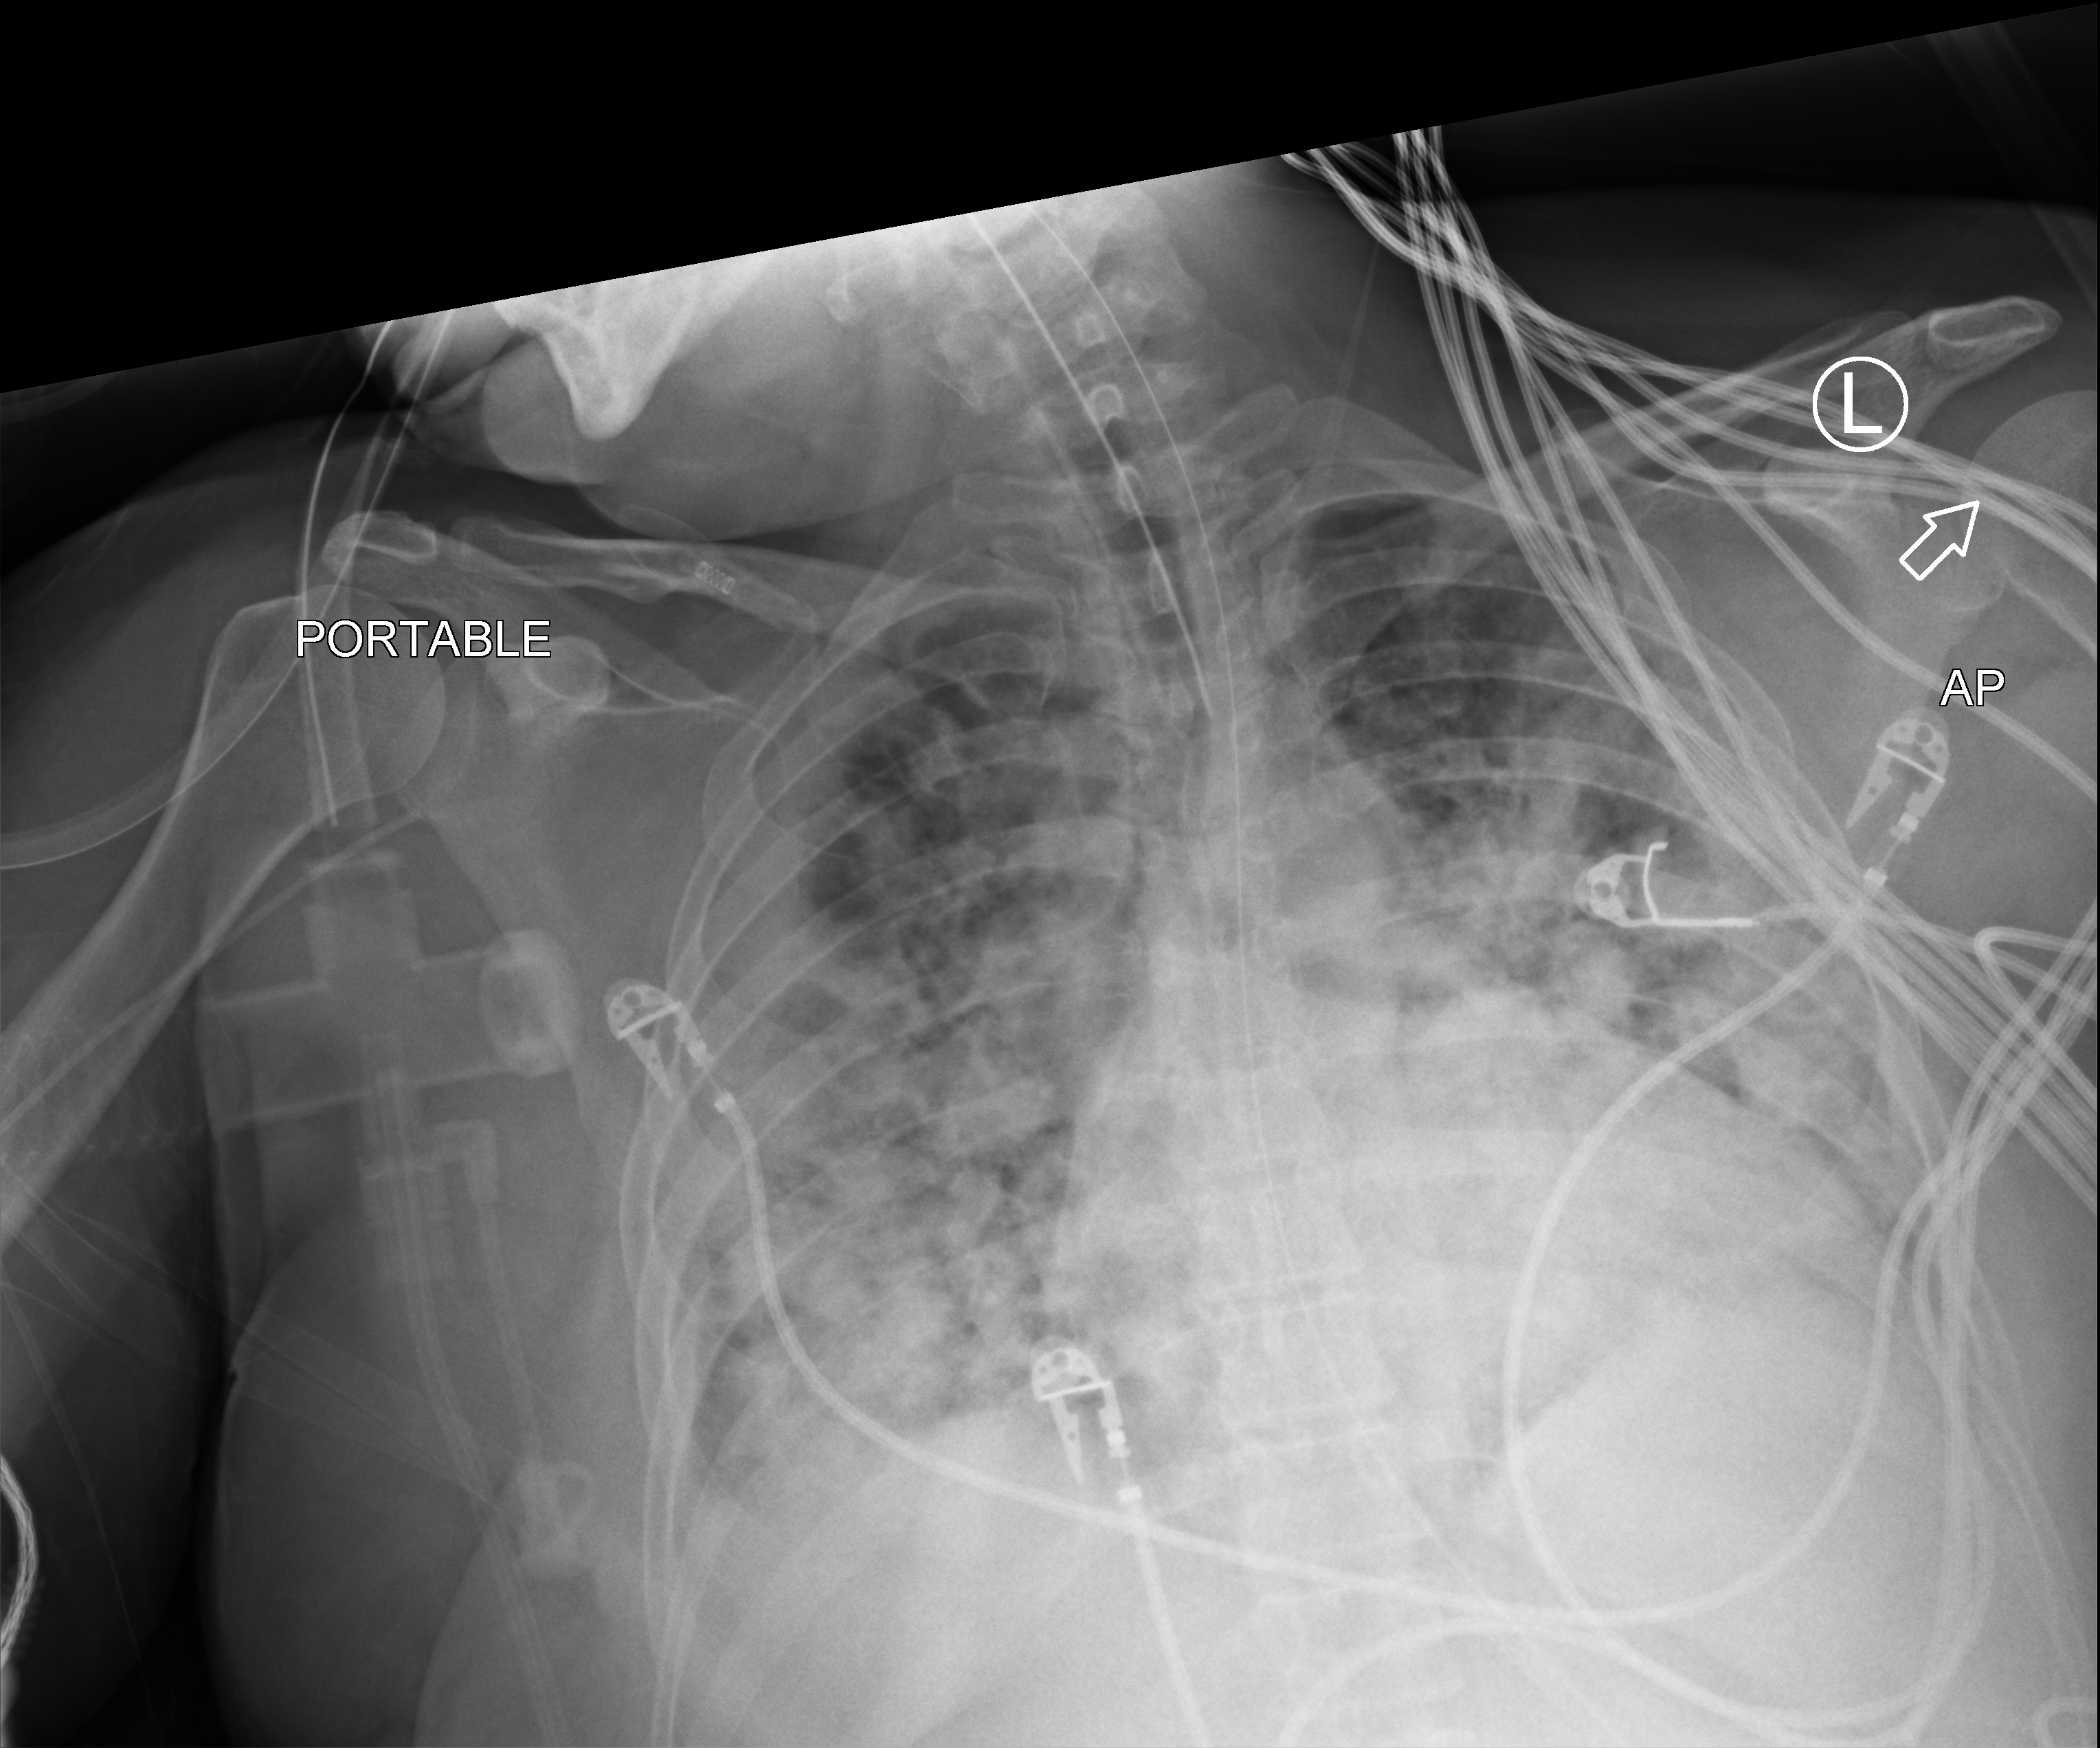
Chest X-ray (portable), anteroposterior (AP) projection. Female patient hospitalised with COVID-19, age 18–59 years.
Hospital-stay facts (about this admission, not read from this image; timing relative to this image not recorded):
- hypertension (admission record): yes
- admitted to intensive care during this hospital stay: yes
- mechanically ventilated during this hospital stay: yes